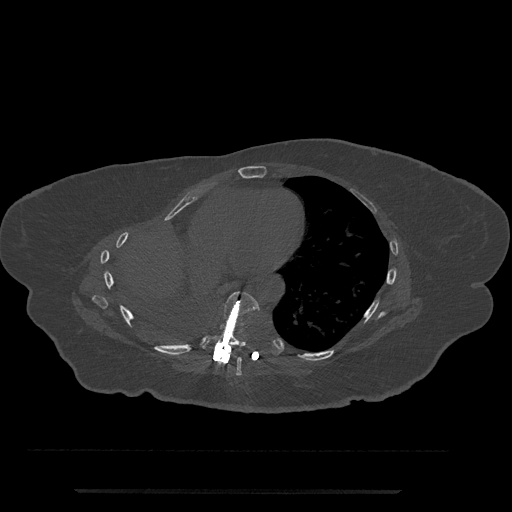
CT including the spine, one axial slice. Position 401 of 797 along the scan axis. 120 kVp. Bone window (W 1800 / L 400 HU). 0.5 mm slice thickness. 512 × 512 image matrix, field of view 440 × 440 mm. Patient: female, 51 years. Case-level facts recorded for this patient, not image findings: primary cancer: neuro; vertebrae with lytic lesions (as recorded): T8.
Annotated regions visible in this slice (semi-automatic segmentation, software-assisted and operator-edited):
- T7 vertebra: bounding box <233,358,242,376> (left, top, right, bottom; pixels)
- T8 vertebra: <202,291,260,352>